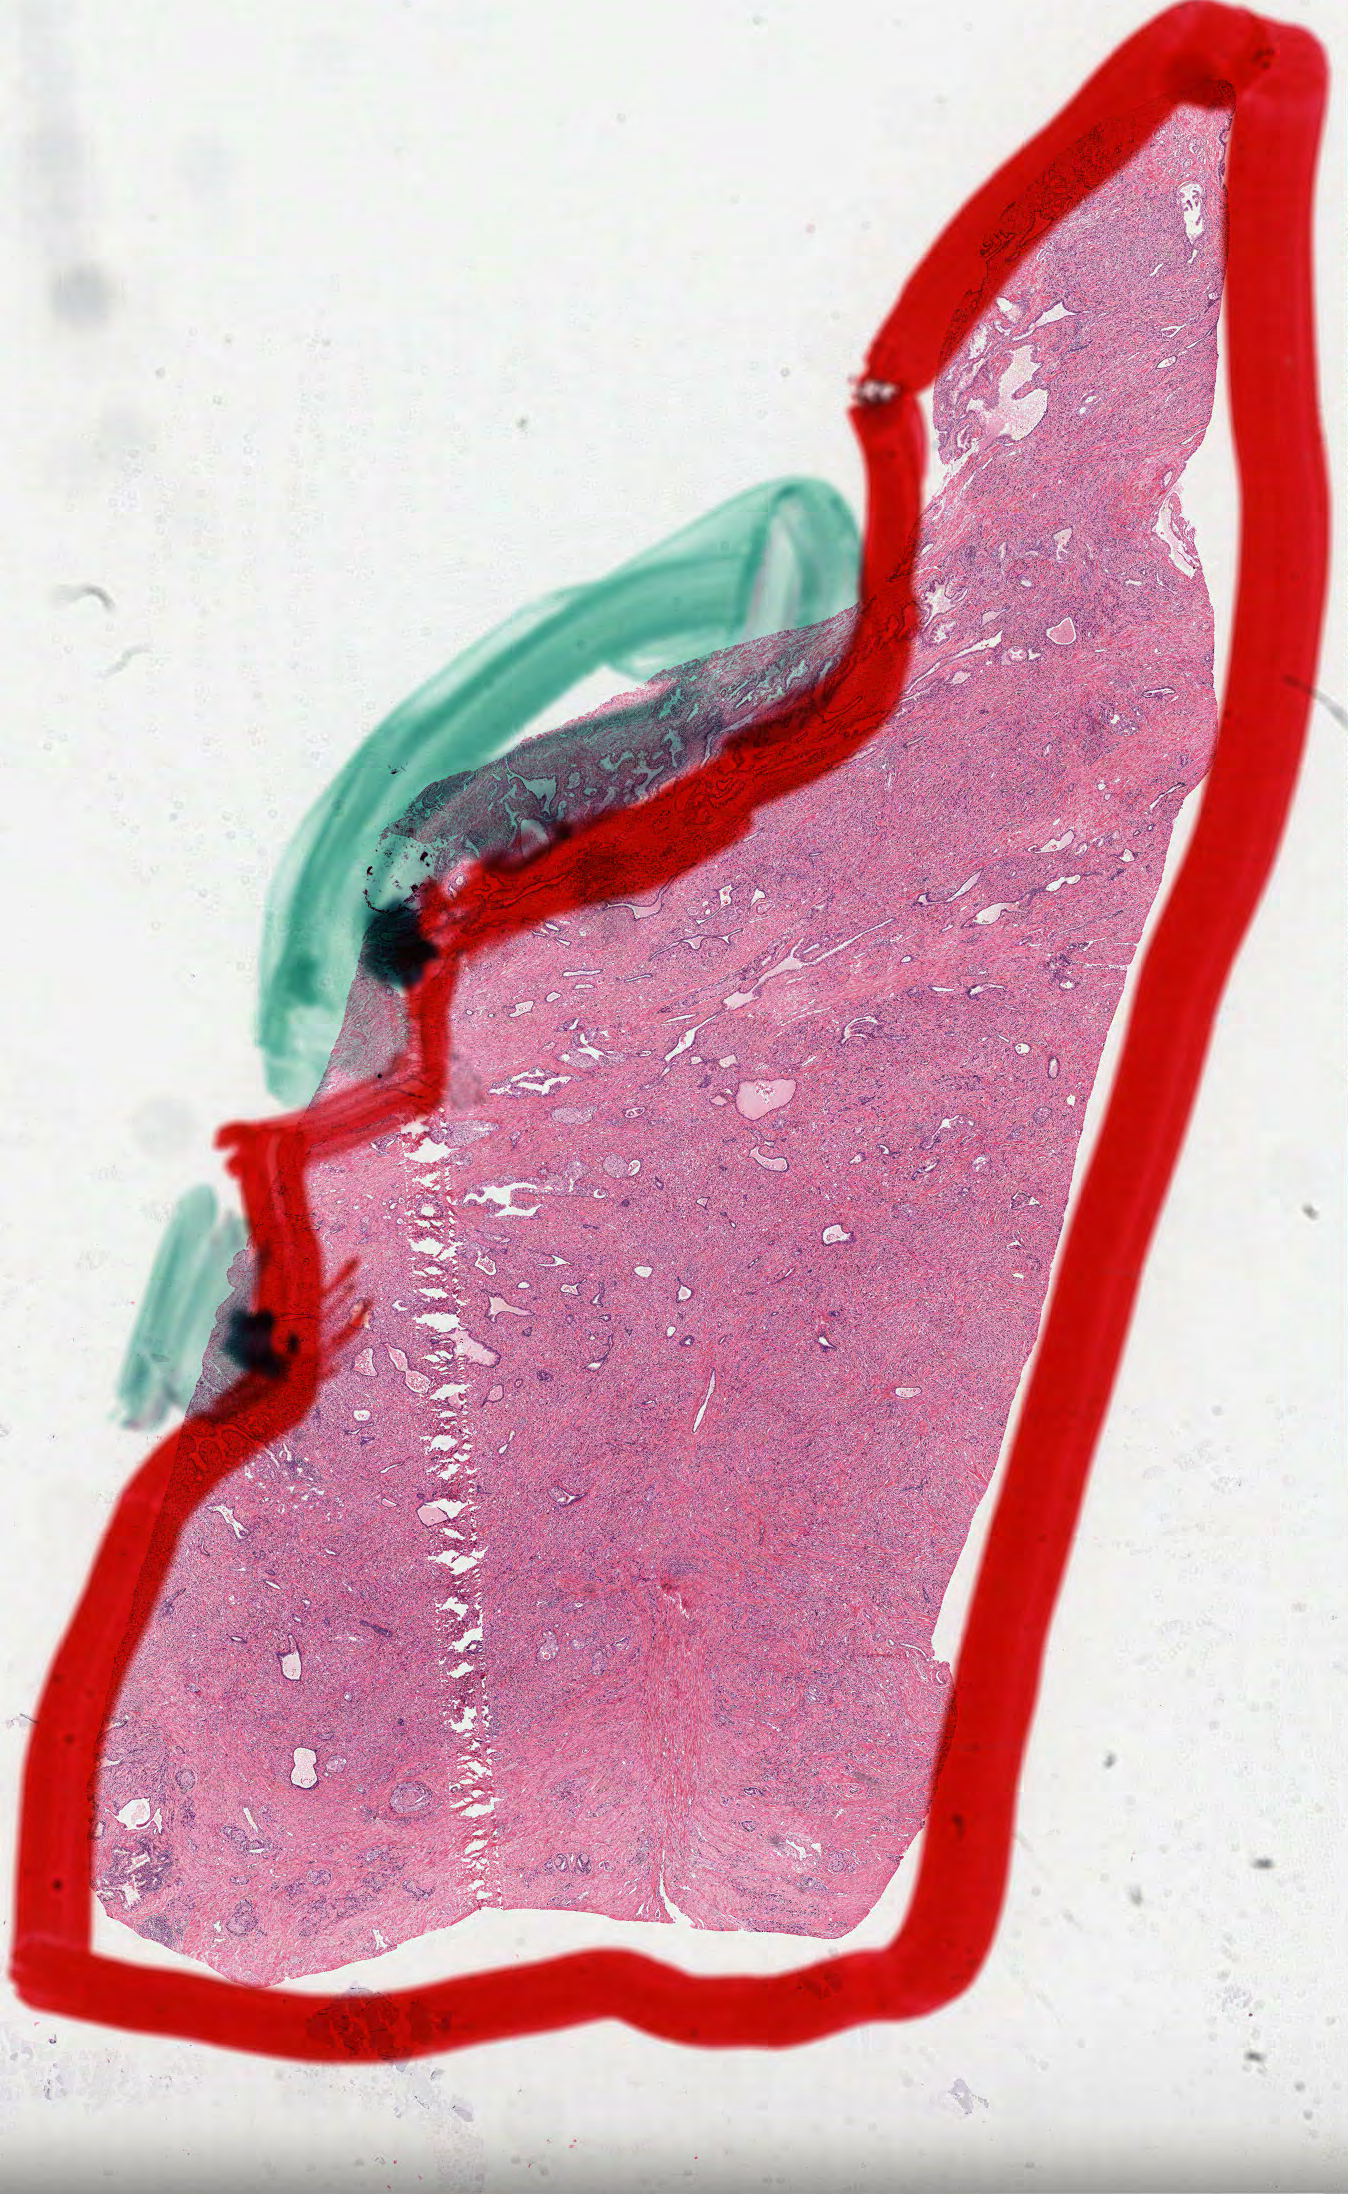
Digitized H&E tissue section (whole slide), shown as a low-resolution overview of the whole scanned area (about 10.9 x 17.7 mm); formalin-fixed paraffin-embedded (FFPE) diagnostic section; sample: primary tumour, prostate. Patient: male, age at initial diagnosis 62 years. Gleason score: 9 (4+5).
• pathologic diagnosis: Acinar cell carcinoma (prostate gland)
• lymph nodes positive (case pathology): 0 of 3 examined